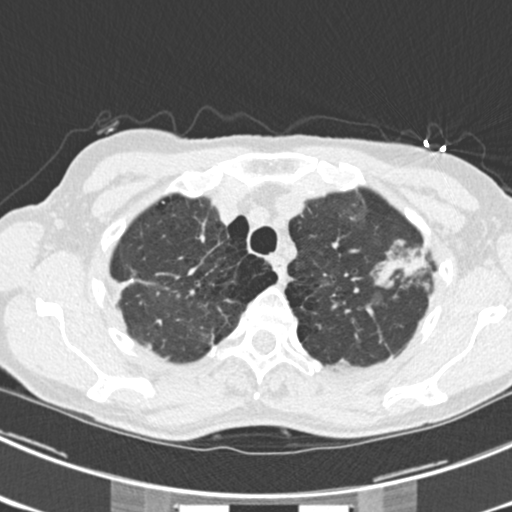
Low-dose screening chest CT, one axial slice. 120 kVp. Lung window (W 1500 / L -600 HU). 2 mm slice thickness. 512 × 512 image matrix, field of view 302 × 302 mm.
Structures marked on this image (outlined manually by an expert reader):
- lesion 1 (tumor, upper lobe of left lung): bounding box [x1, y1, x2, y2] px = [376, 250, 428, 287]